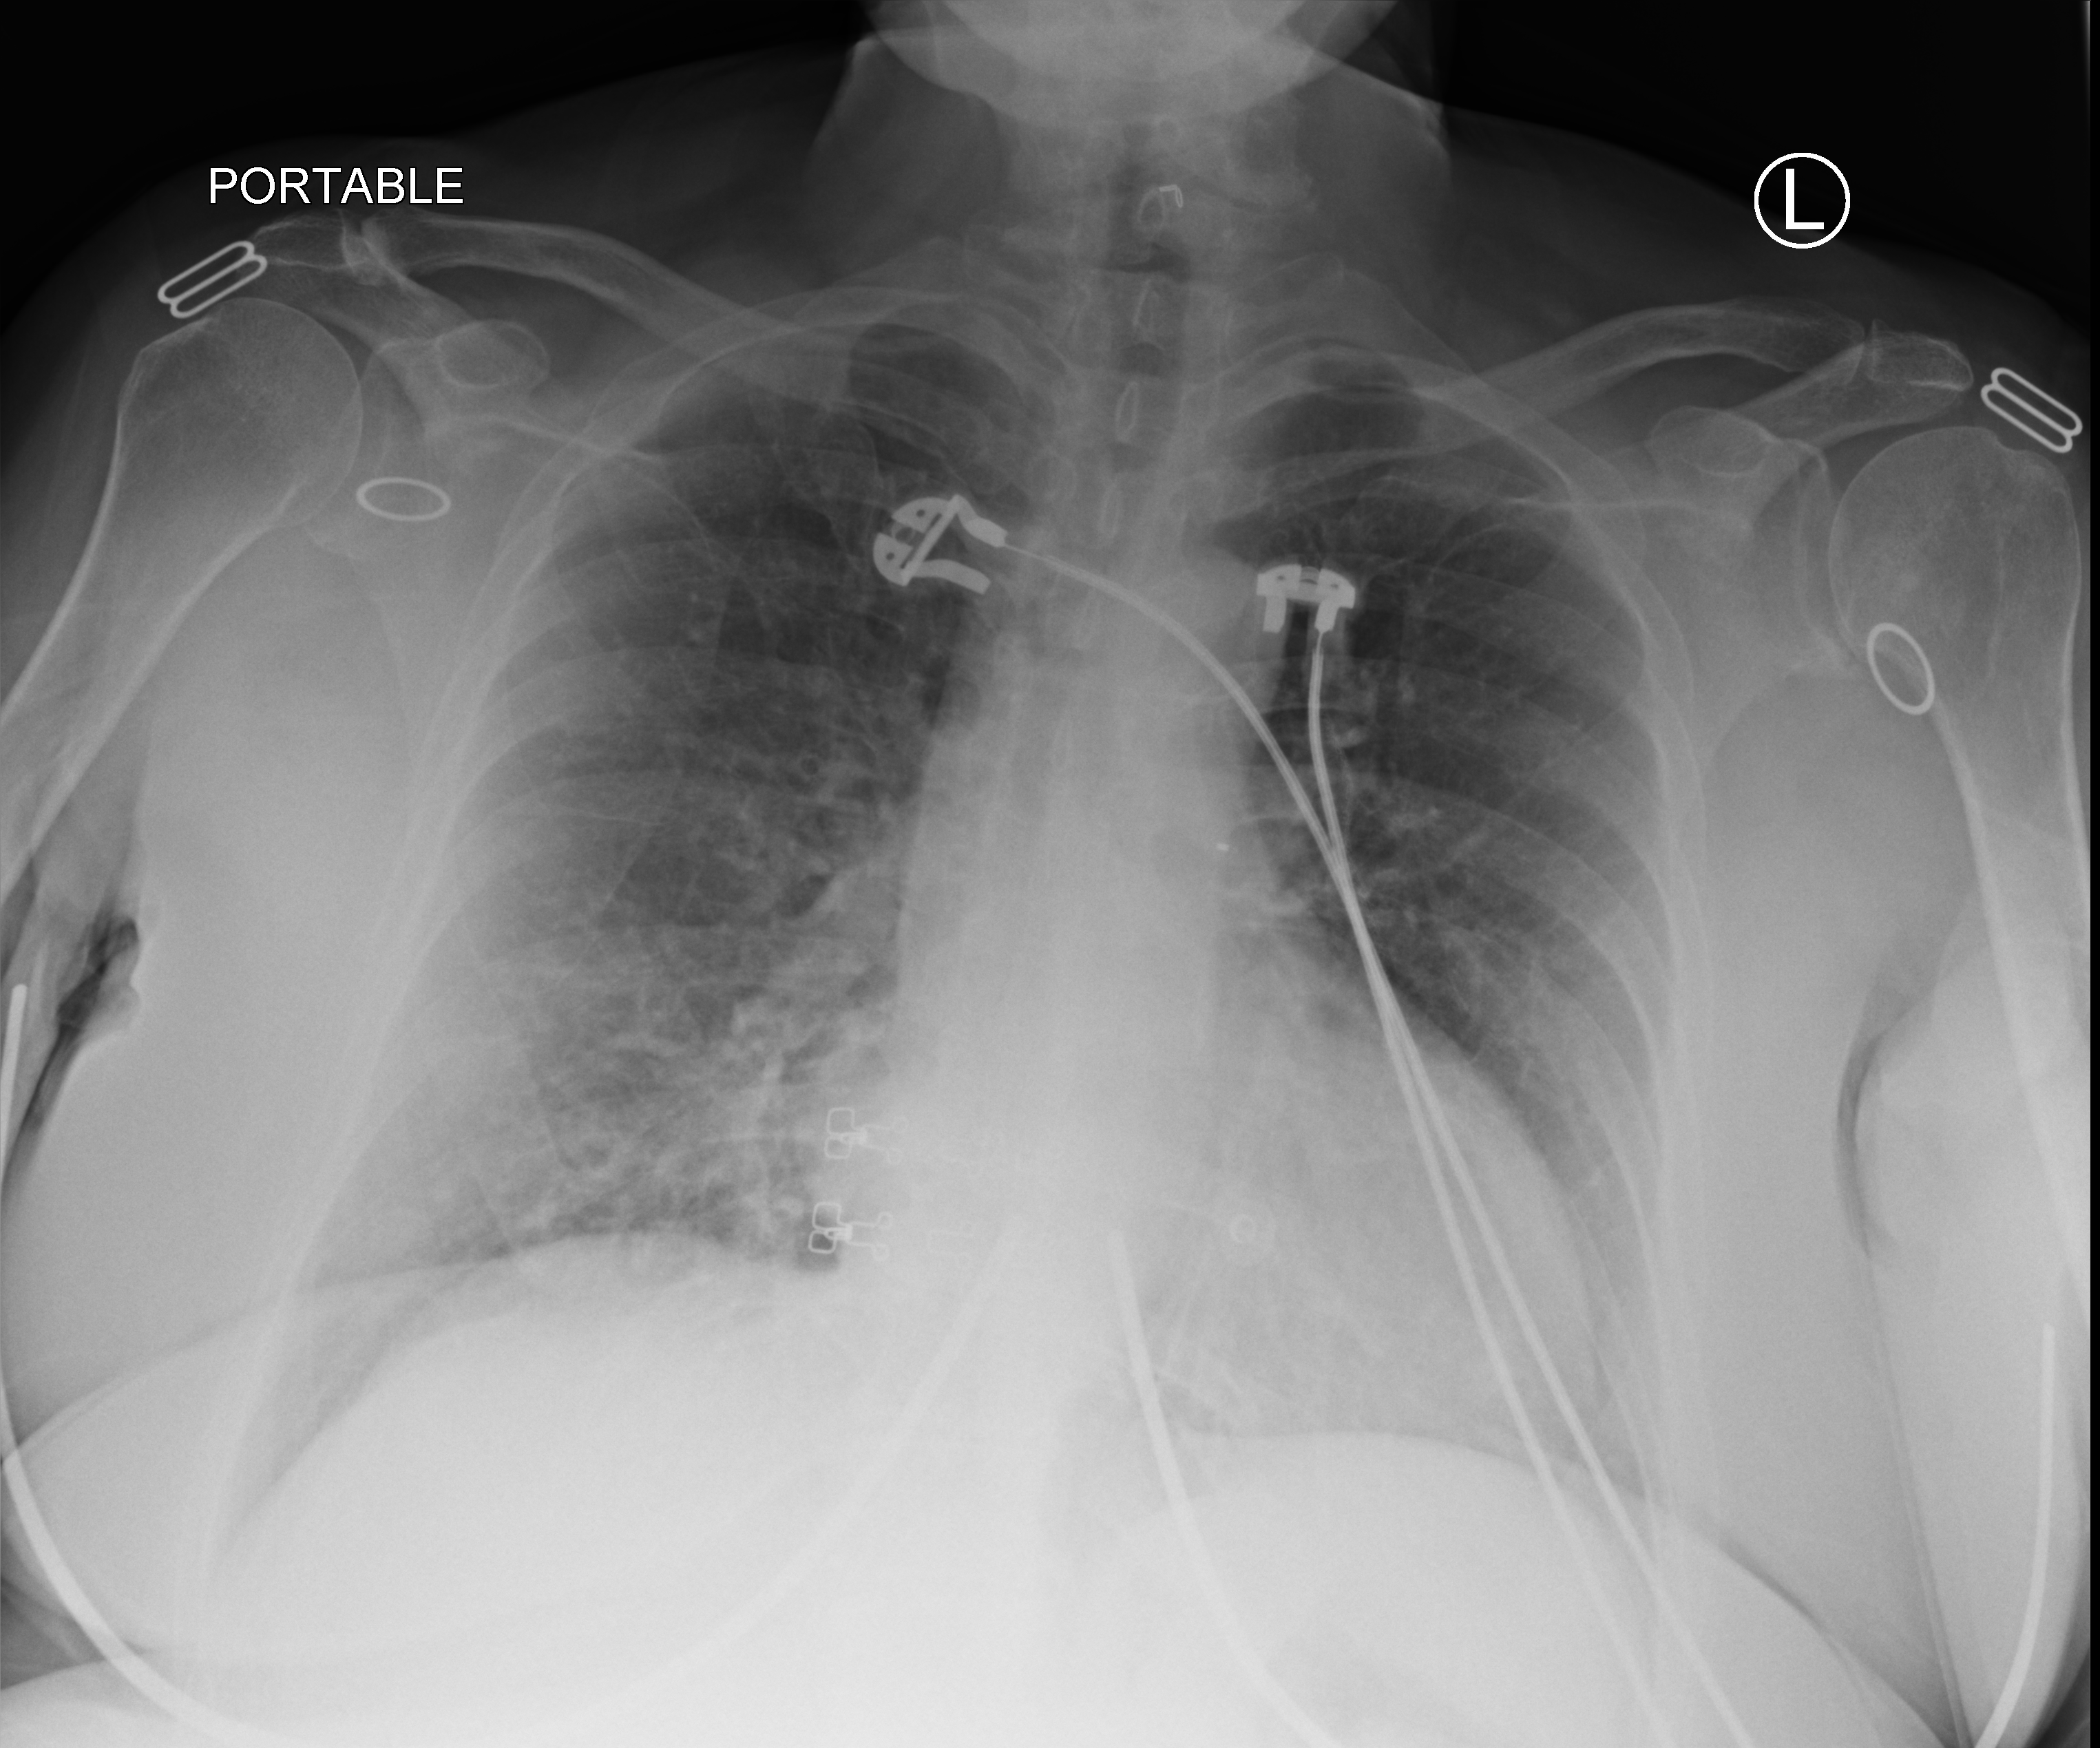
Chest X-ray (portable), anteroposterior (AP) projection. Female patient hospitalised with COVID-19, age 60–74 years.
Admission-level facts for this patient (not findings on this image; timing relative to this image not recorded):
- mechanically ventilated during this hospital stay: no
- admitted to intensive care during this hospital stay: no